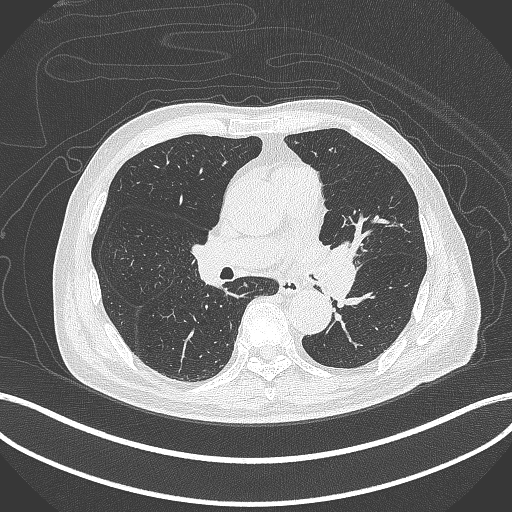
Chest CT, one axial slice. Slice 231 of 417 in the series (ordered by position). Lung window (W 1500 / L -600 HU). 1 mm slice thickness. 512 × 512 image matrix. Male patient, age 77 years. From the clinical record (not read from this slice): clinical TNM (as recorded): T3 N1 M0.
Annotated regions visible in this slice (rectangle marked by the reading radiologist):
- lung tumour (recorded histology: adenocarcinoma): bounding box <310,237,361,314> (left, top, right, bottom; pixels)